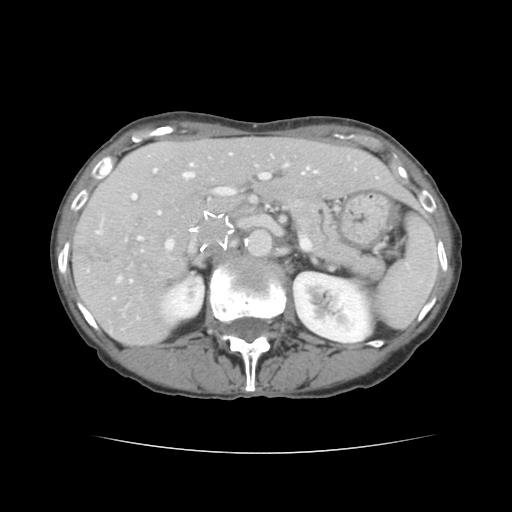
Contrast-enhanced abdominal CT, one axial slice; position 82 of 136 along the scan axis; 120 kVp; intravenous contrast given; soft-tissue window (W 400 / L 40 HU); 512 × 512 image matrix, field of view 319 × 319 mm. Female patient, age 77 years. From the clinical record (not read from this slice): diagnosis: colorectal cancer liver metastases, imaged before liver resection; multiple liver metastases: yes.
Structures marked on this image (outlined manually by an expert reader):
- hepatic veins: bounding box (x1, y1, x2, y2) in pixels: (139, 153, 317, 239)
- liver: (74, 137, 413, 345)
- planned liver remnant (the part of the liver to remain after resection): (154, 137, 412, 211)
- portal vein (with intrahepatic branches): (97, 164, 288, 282)